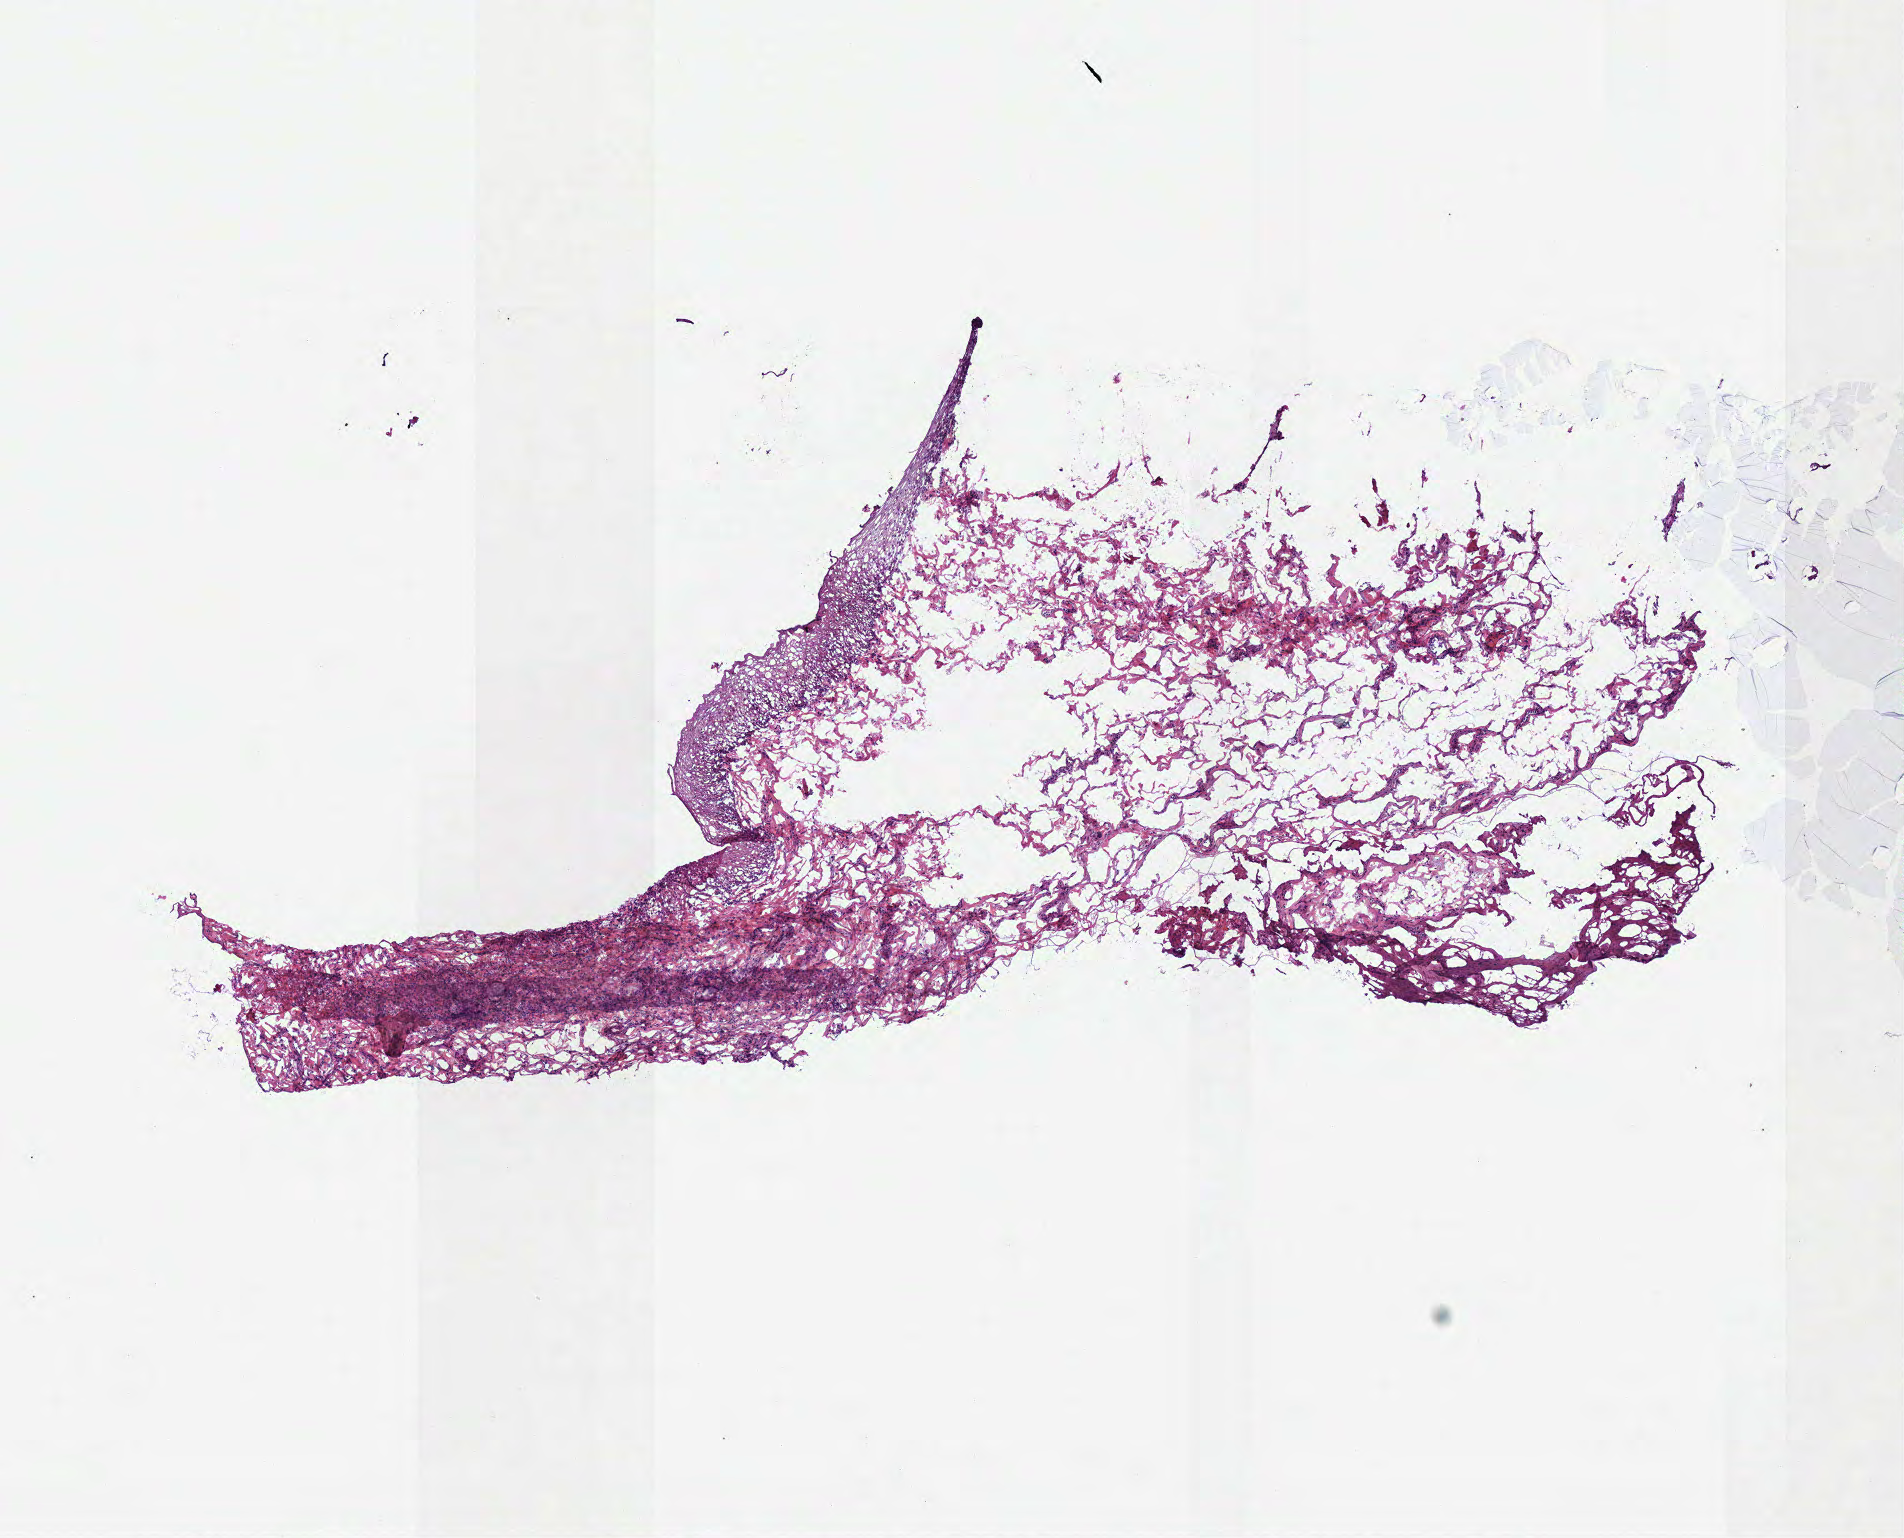
Hematoxylin and eosin (H&E) stained whole-slide image — low-resolution overview of the scanned area, about 7.5 x 6.1 mm (from a 40x scan), frozen section from the top of the tissue portion, sample: solid tissue normal (non-tumour tissue), head and neck. Male patient; age at initial diagnosis 68 years.
- this section: solid tissue normal sample (biorepository sample class)
- patient diagnosis: Squamous cell carcinoma, NOS (floor of mouth, NOS)